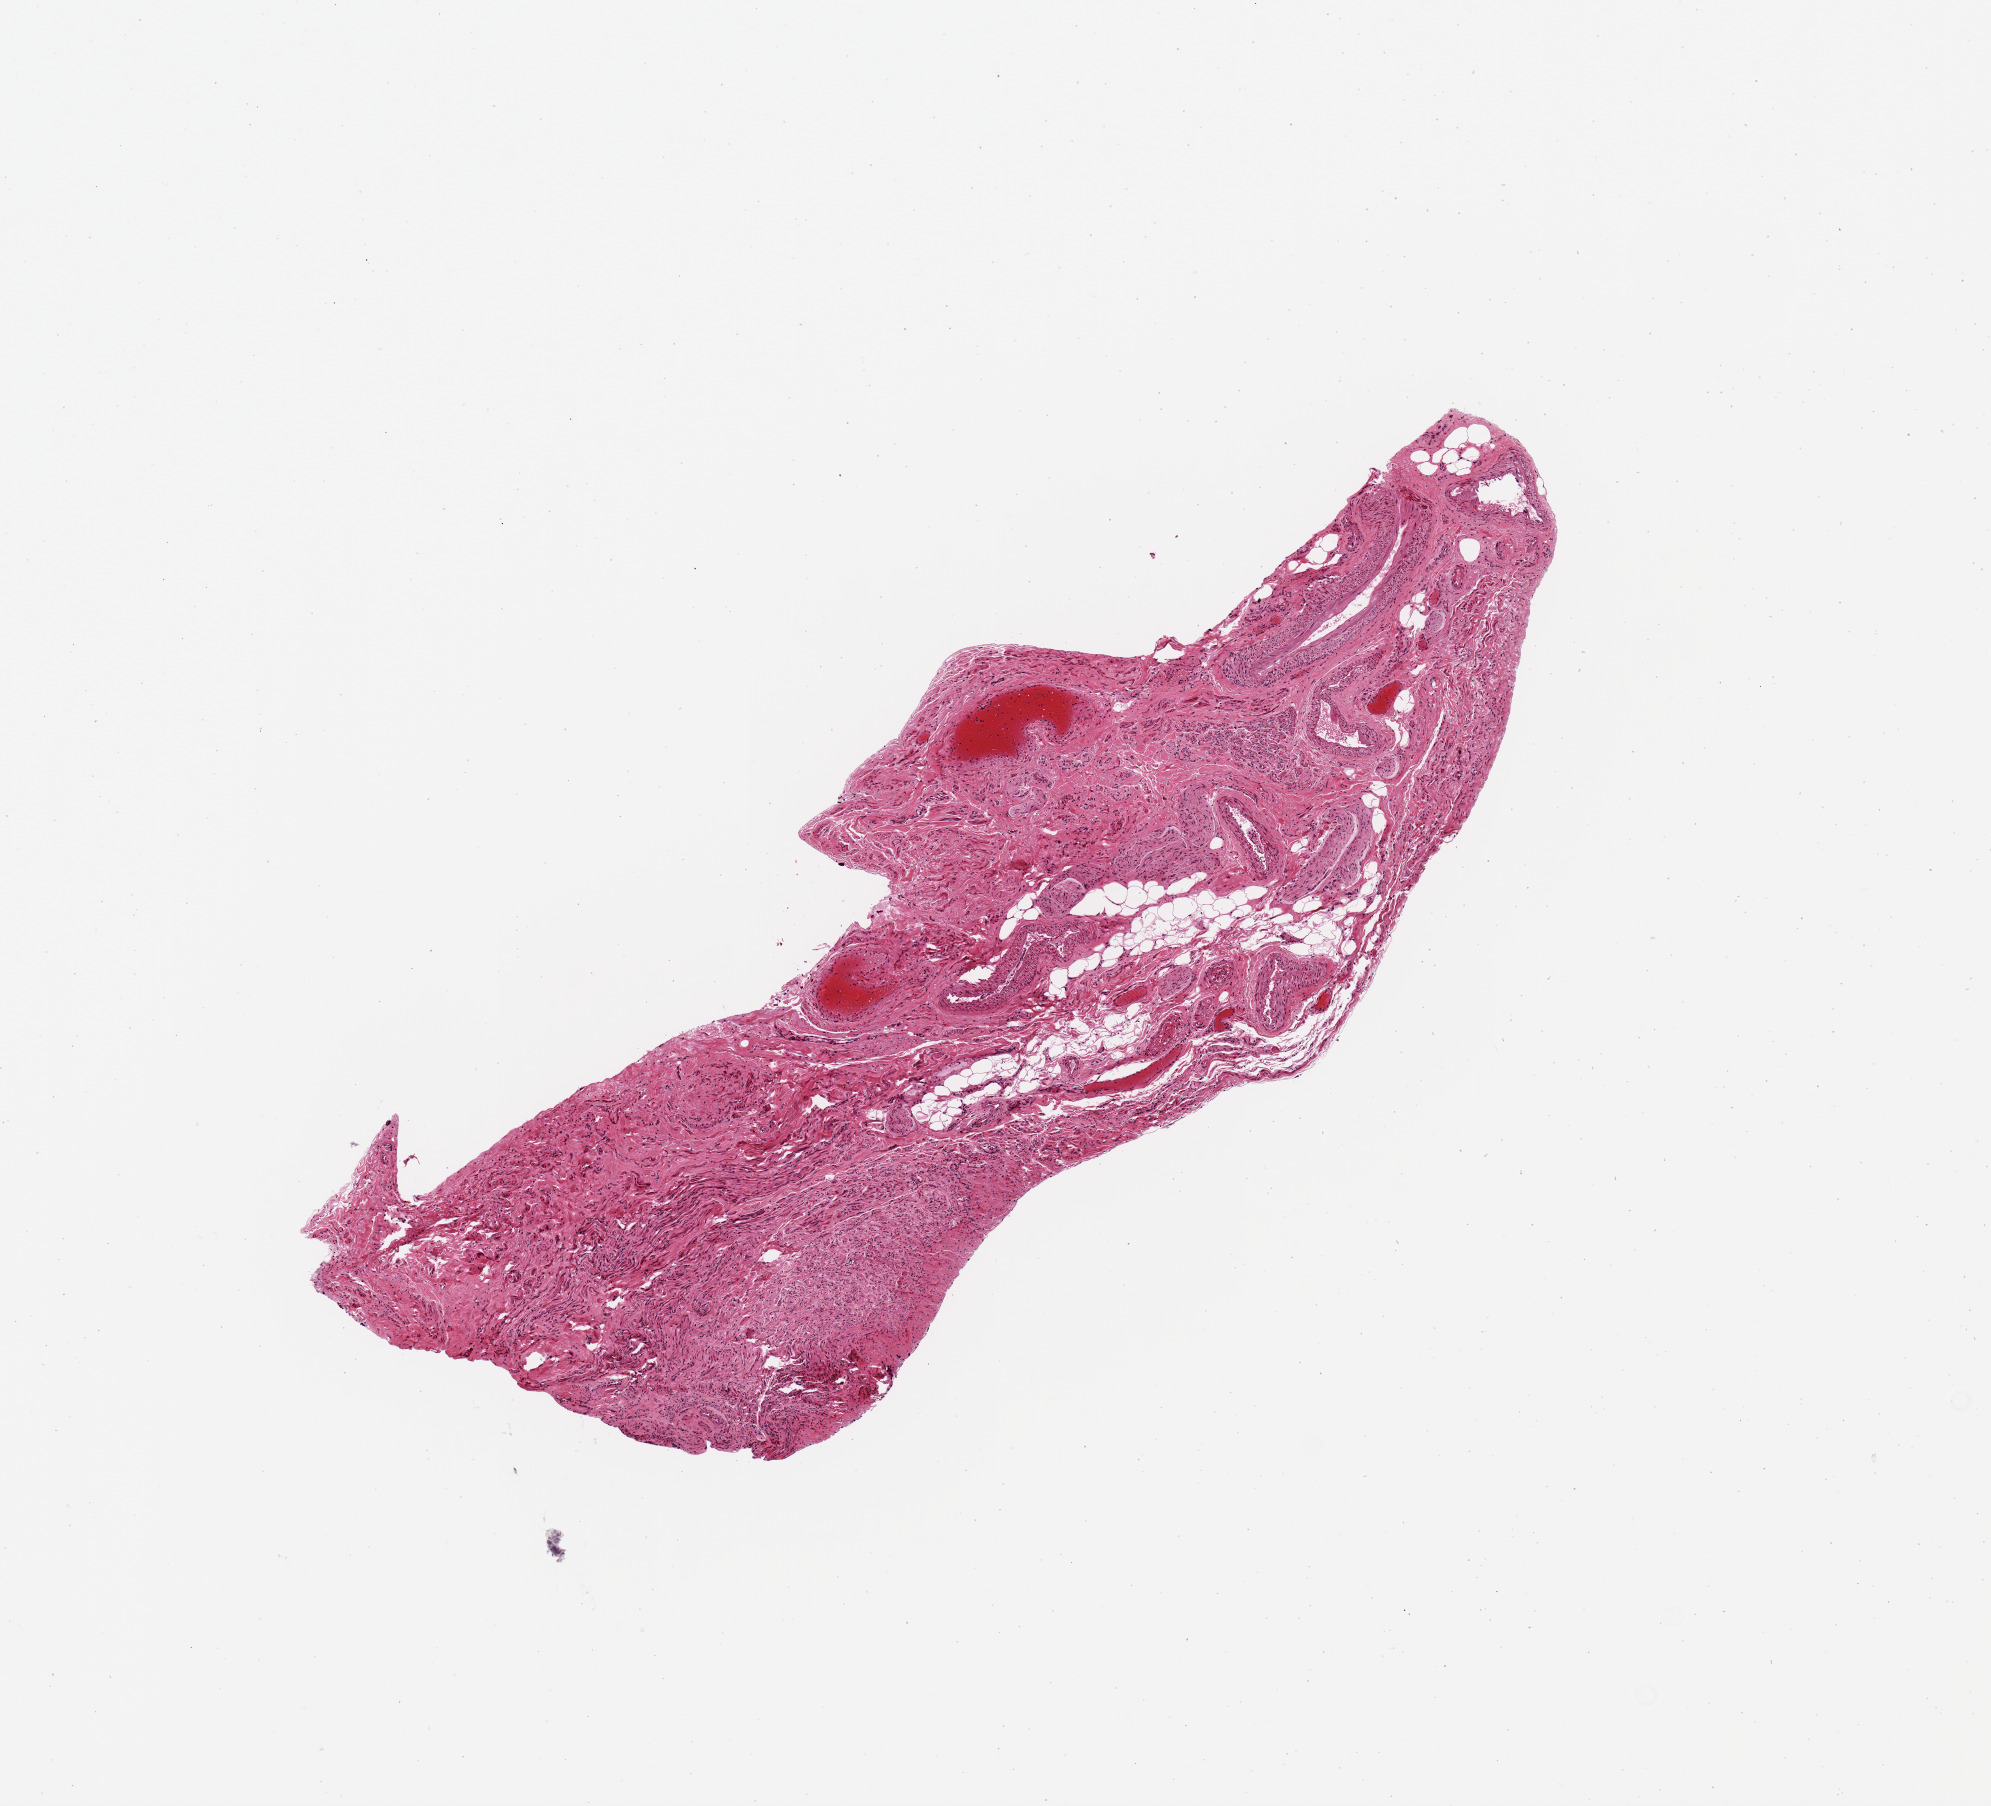
Hematoxylin and eosin (H&E) whole-slide image, brightfield — shown as a low-resolution overview of the whole scanned area (about 7.9 x 7.1 mm); PAXgene-fixed, paraffin-embedded tissue; target tissue: ovary; donor tissue sample. Donor: female.
Review note (as recorded): Not ovary: fibrovascular, adipose, and neural tissue.